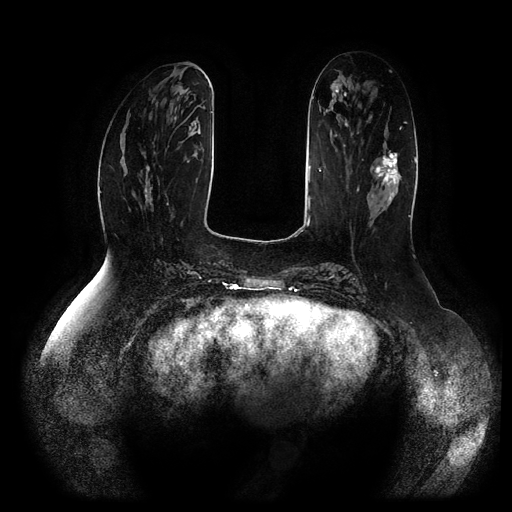
Breast MRI (dynamic contrast-enhanced, multi-phase), one axial slice. Slice 36 of 116 in the series (ordered by position). Dynamic contrast-enhanced series, time point 2 of 5 at this slice position (early post-contrast). 1.5 T. TE 2.5 ms, TR 5.2 ms. 2 mm slice thickness. 512 × 512 image matrix. Patient: female, 66 years.
Annotated regions visible in this slice (semi-automatic segmentation, software-assisted and operator-edited):
- breast lesion (labelled 'tumour' in the annotation; benign lesions carry a separate 'benign' label): bounding box [x1, y1, x2, y2] px = [372, 150, 401, 202]